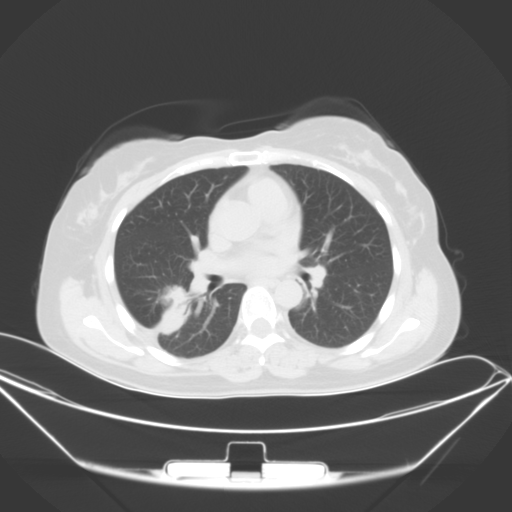
Chest CT, one axial slice. Slice 22 of 46 in the series (ordered by position). 120 kVp. Lung window (W 1500 / L -600 HU). 5 mm slice thickness. 512 × 512 image matrix, field of view 407 × 407 mm. Female patient, age 42 years. From the clinical record (not read from this slice): clinical TNM (as recorded): T1c N0 M1a.
Annotated regions visible in this slice (bounding box drawn by a radiologist):
- lung tumour (recorded histology: adenocarcinoma): bounding box (x1, y1, x2, y2) in pixels: (146, 285, 200, 340)